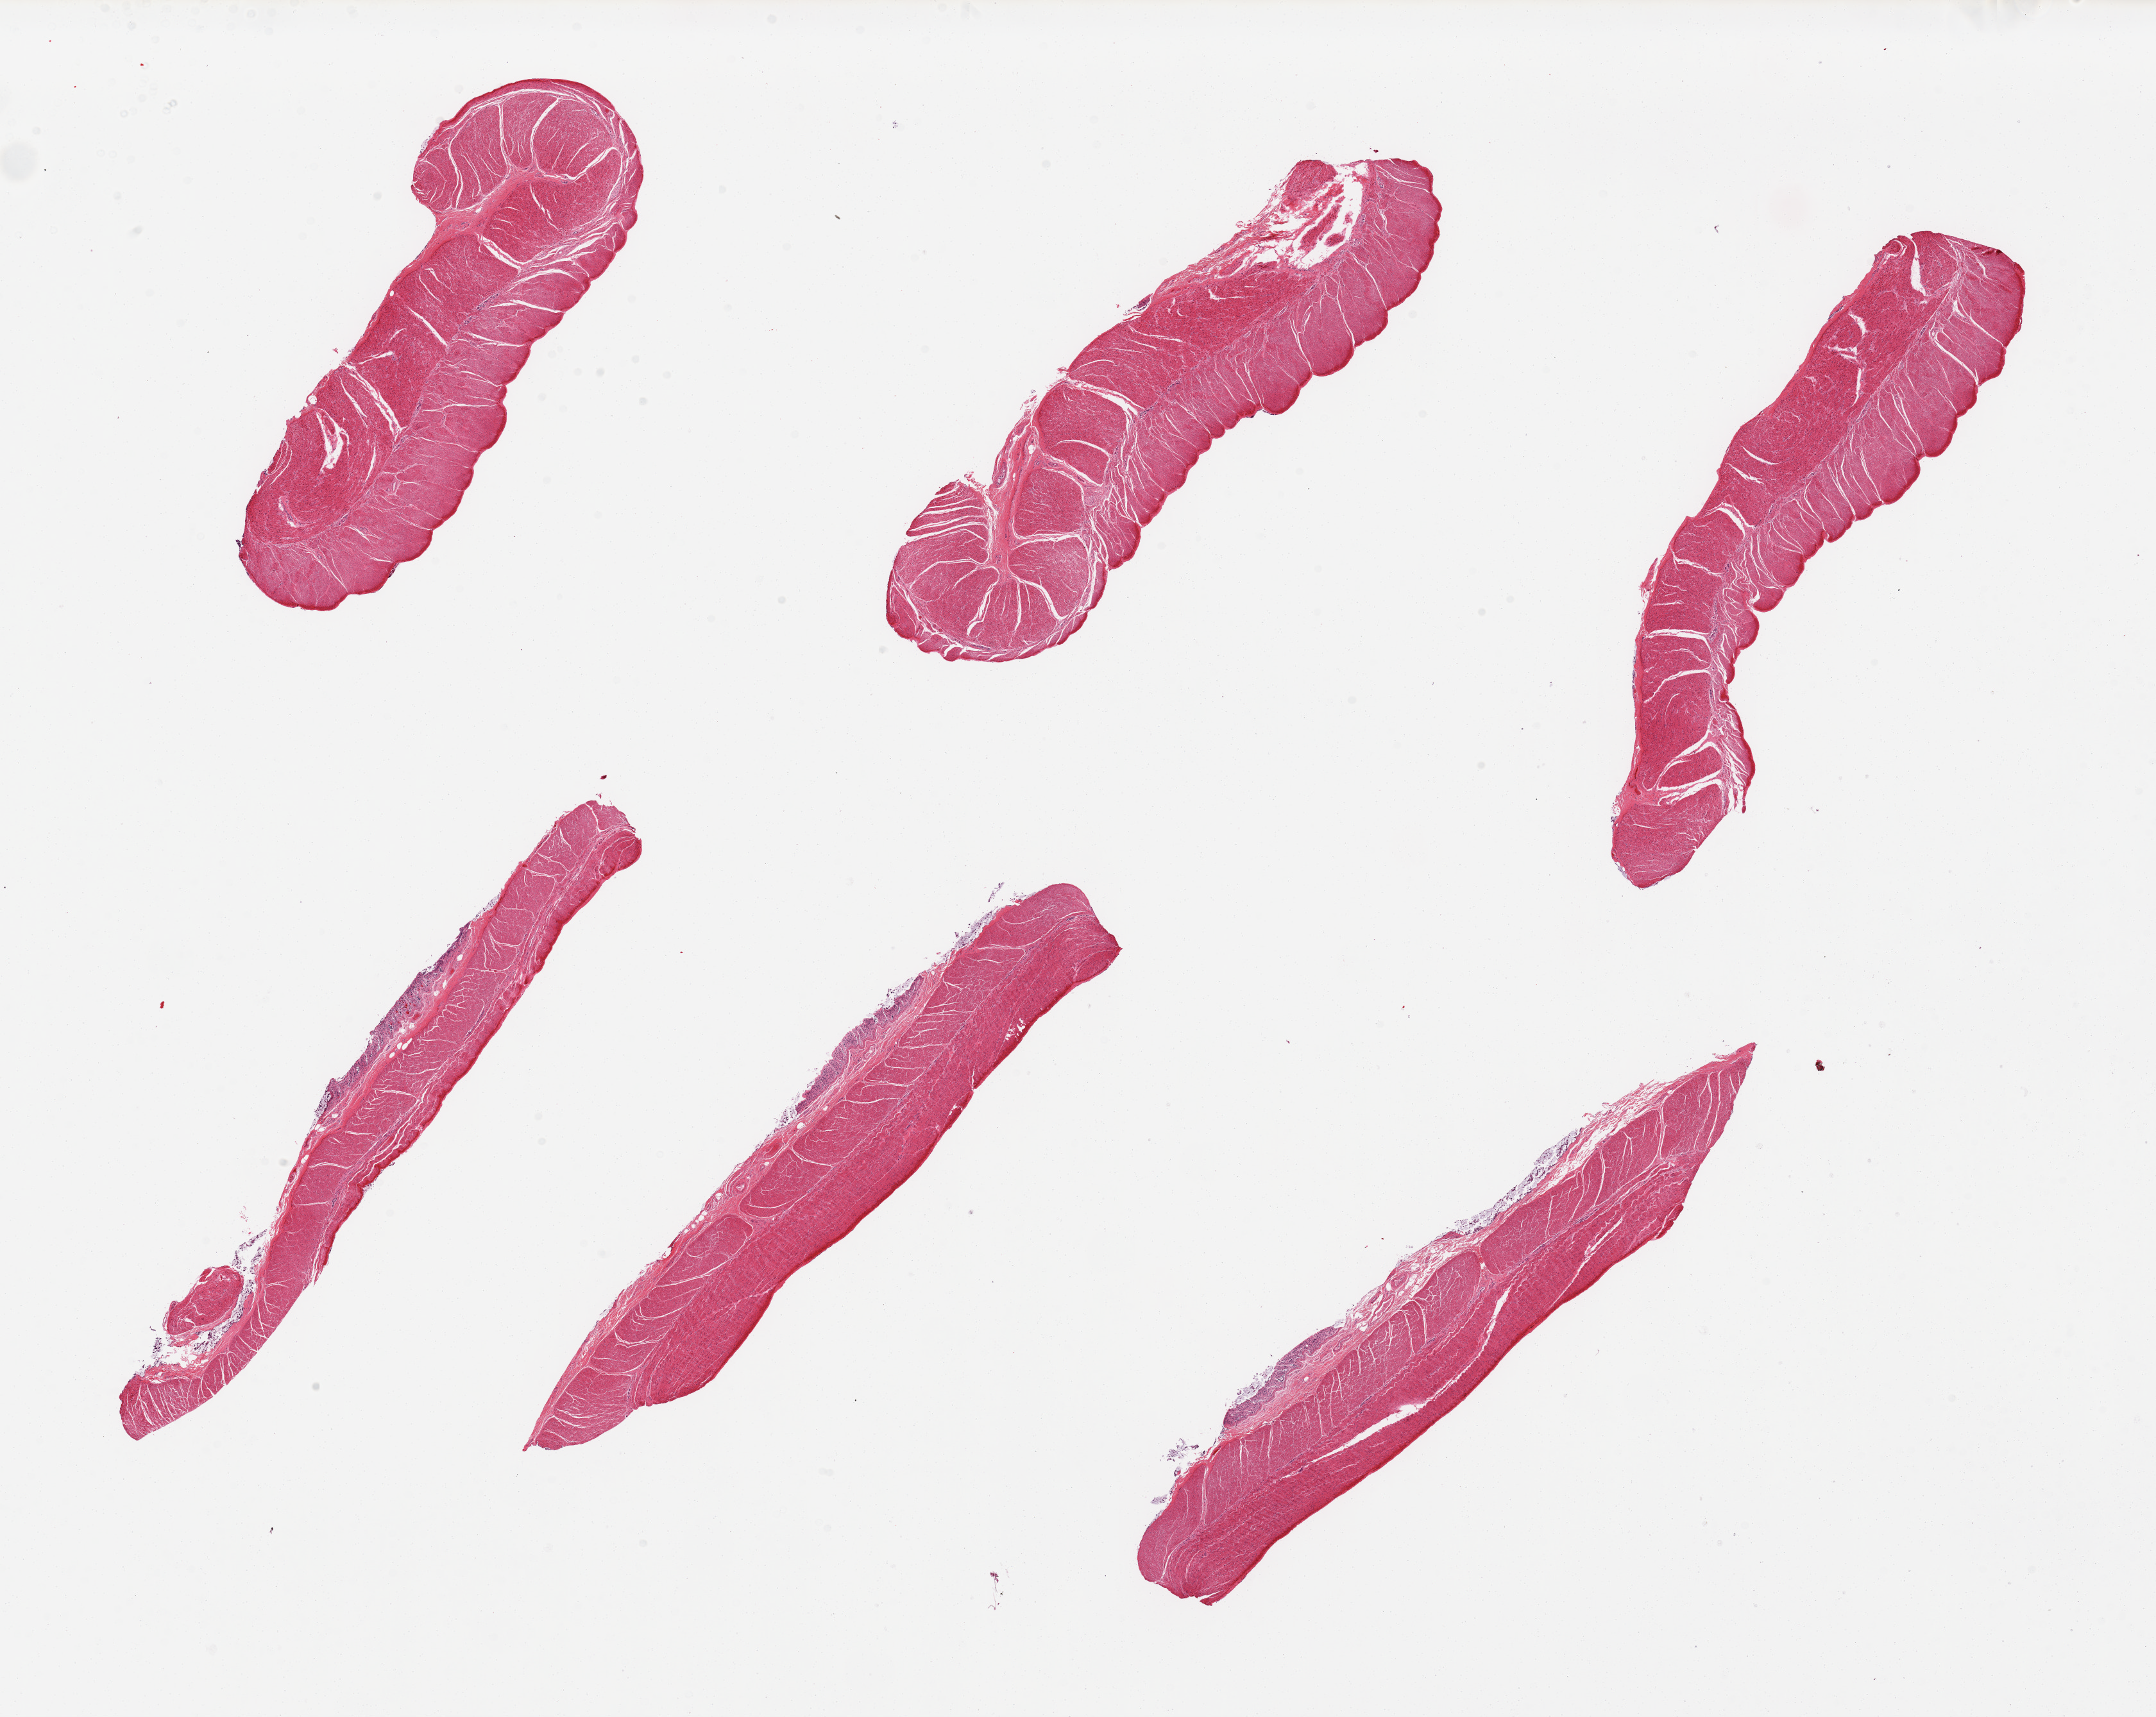
Digitized hematoxylin and eosin (H&E)-stained section, brightfield, shown as a low-resolution overview of the whole scanned area (about 26.6 x 21.2 mm, from a 20x scan); PAXgene-fixed, paraffin-embedded tissue; target tissue: sigmoid colon; tissue donor sample. Male donor.
Reviewer comment on this tissue sample: 6 pieces, predominantly muscularis with some residual autolyzed mucosa.